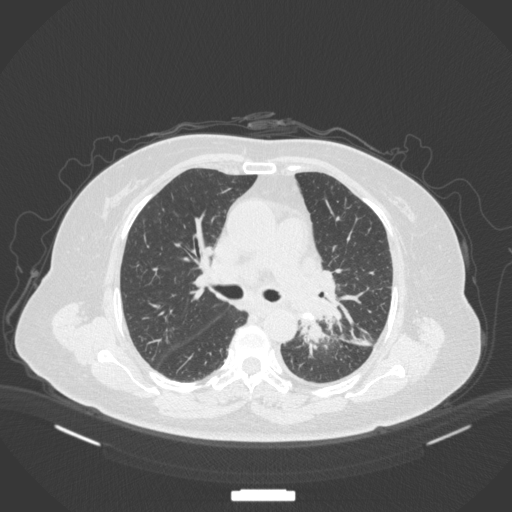
Chest CT, one axial slice; slice 216 of 328 in the series (ordered by position); reconstruction kernel B31f; 120 kVp; lung window (W 1500 / L -600 HU); 512 × 512 image matrix. Patient: female, 69 years. Case-level facts recorded for this patient, not image findings: clinical TNM (as recorded): T2b N3 M1.
Structures marked on this image (bounding box drawn by a radiologist):
- lung tumour (recorded histology: adenocarcinoma): box from (x=290, y=311) to (x=332, y=358) px